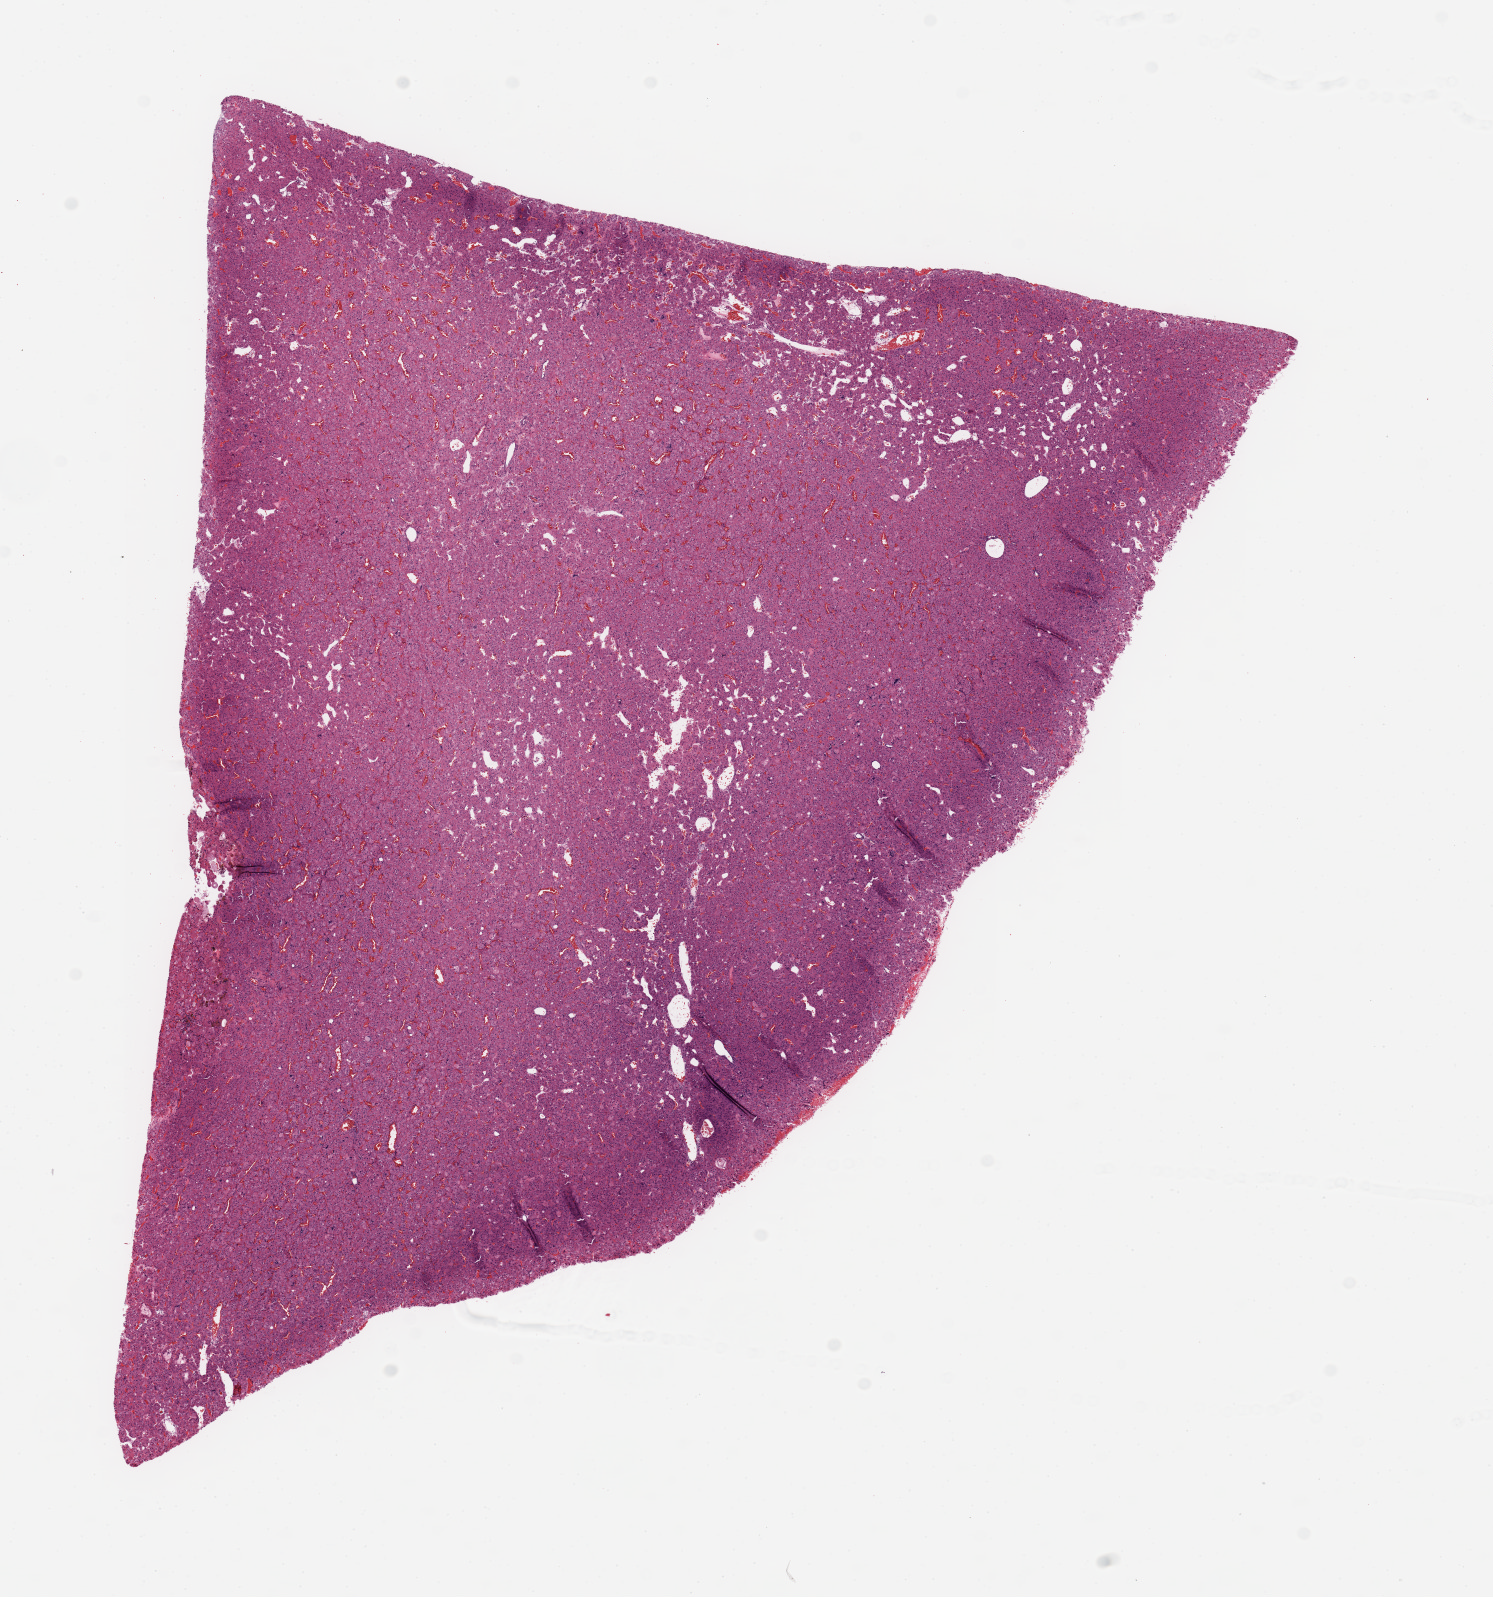
Whole-slide histology image, H&E-stained — a low-resolution overview of the entire scanned area, about 11.8 x 12.6 mm. Tumour tissue sample, kidney. Female, 73 y/o. Histologic grade: G1 (well differentiated).
Diagnosis: Renal cell carcinoma, NOS. AJCC pathologic stage: I.